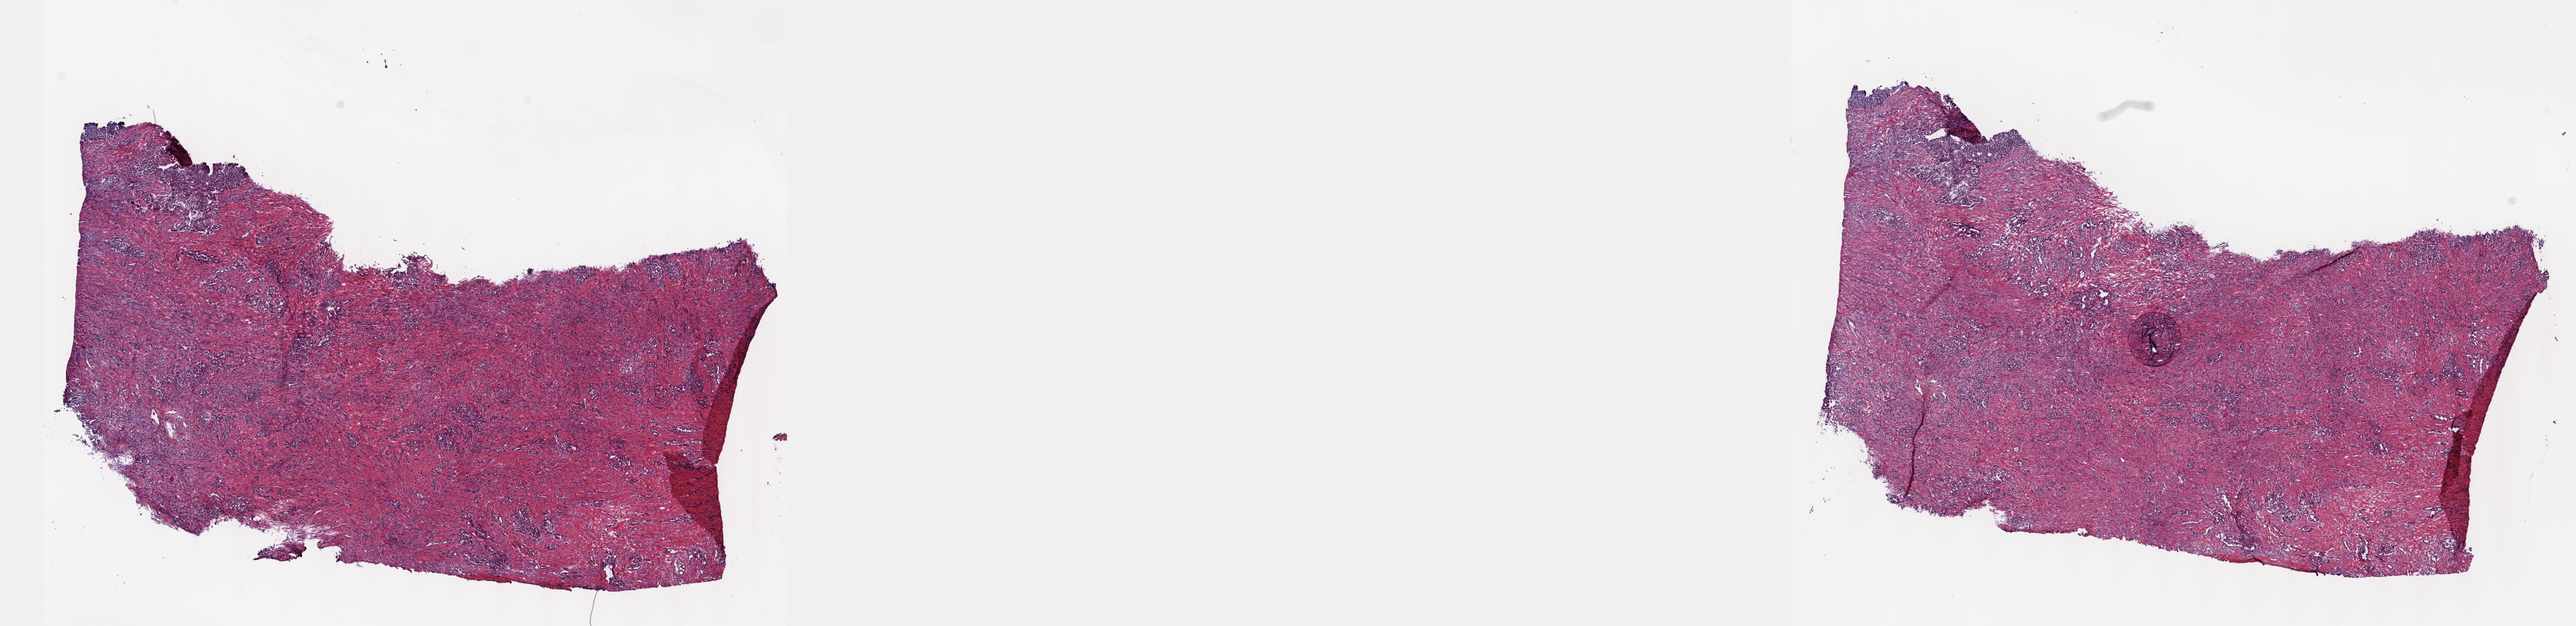
Whole-slide histology image, H&E-stained, whole scanned area (about 29.7 x 7.2 mm, from a 40x scan) shown as a low-resolution overview. Frozen section from the top of the tissue portion. Primary tumour sample from the mesothelium. Male, age 58 years at initial diagnosis. Composition of this section per pathologist review: tumour cells 100%, tumour nuclei 70%, normal cells 0%, stromal cells 0%, necrosis 0%. Infiltration values recorded for this section: lymphocyte infiltration 0%, monocyte infiltration 0%, neutrophil infiltration 0%.
• pathologic diagnosis: Epithelioid mesothelioma, malignant (pleura, NOS)
• TNM: T4 N1 MX
• AJCC pathologic stage: IV (6th edition)